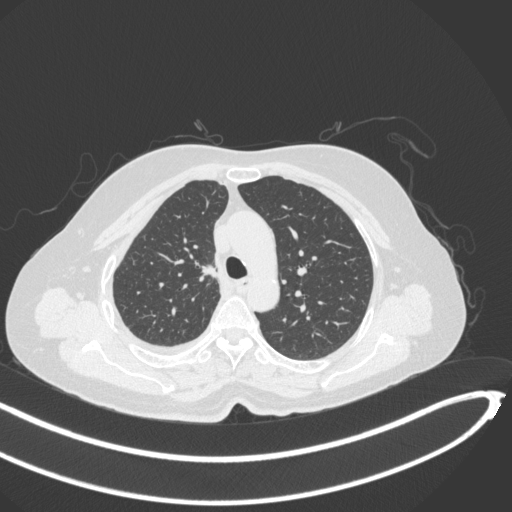
Chest CT, one axial slice; position 219 of 297 along the scan axis; 120 kVp; lung window (W 1500 / L -600 HU); 1 mm slice thickness; 512 × 512 image matrix, field of view 400 × 400 mm. Patient: female, 64 years. From the clinical record (not read from this slice): clinical TNM (as recorded): T1b N0 M1.
Outlined on this slice (rectangle marked by the reading radiologist):
- lung tumour (recorded histology: adenocarcinoma): bounding box <193,256,221,286> (left, top, right, bottom; pixels)